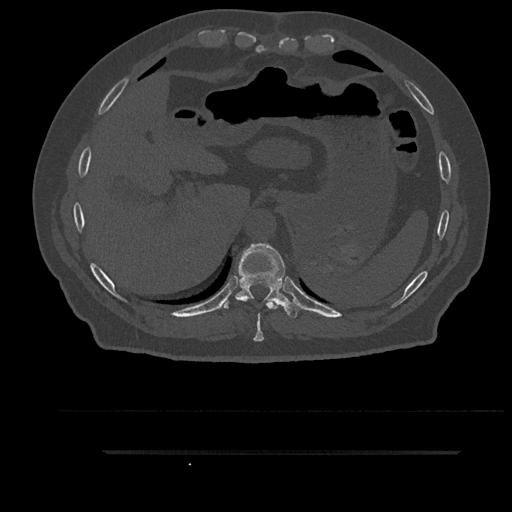
CT including the spine, one axial slice. Reconstruction kernel Br40s/3. Bone window (W 1800 / L 400 HU). 512 × 512 image matrix, field of view 432 × 432 mm. Male patient, age 63 years. From the clinical record (not read from this slice): primary cancer: renal.
Structures marked on this image (semi-automatically segmented with operator editing):
- T10 vertebra: bounding box [x1, y1, x2, y2] px = [222, 243, 302, 318]
- T9 vertebra: [254, 300, 278, 342]